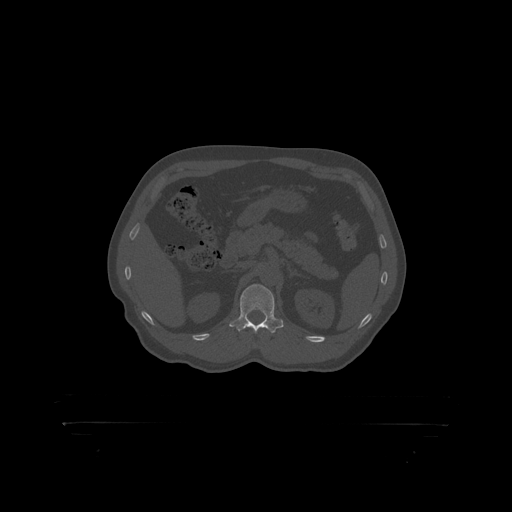
CT including the spine, one axial slice. Position 328 of 399 along the scan axis. Reconstruction kernel STANDARD. 120 kVp. Bone window (W 1800 / L 400 HU). 1.25 mm slice thickness. 512 × 512 image matrix, field of view 650 × 650 mm. Patient: male, 46 years. From the clinical record (not read from this slice): primary cancer: skin.
Structures marked on this image (semi-automatically segmented with operator editing):
- L1 vertebra: box from (x=240, y=285) to (x=275, y=319) px